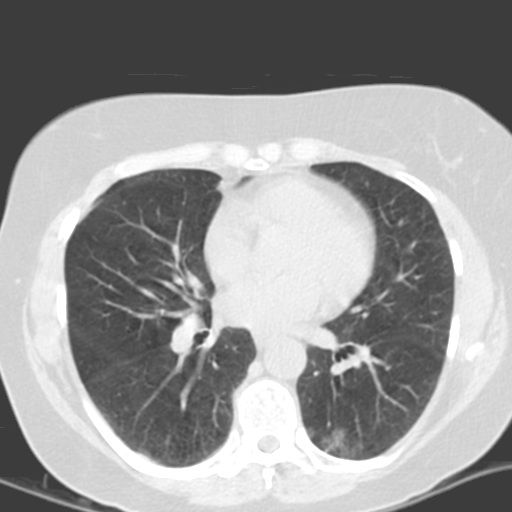
Low-dose screening chest CT, axial slice; second screening round (one year after baseline); lung window (W 1500 / L -600 HU); standard (soft-tissue) reconstruction kernel (B); 120 kVp; slice 77 of 161 in the series. Female participant, aged 55 years at enrolment. Current smoker at enrolment.
Lesion marked by an expert reader, bounding box (x1, y1, x2, y2) in pixels: (305, 411, 378, 466). The screening reader recorded 4 non-calcified nodules or masses ≥4 mm on this exam; which of them this box marks is not recorded. Official screen result: positive, other. Later outcome: lung cancer diagnosed 688 days after this screen — adenocarcinoma with mixed subtypes, left lower lobe, poorly differentiated (G3), stage IA (AJCC 6th edition), 21 mm at pathology.